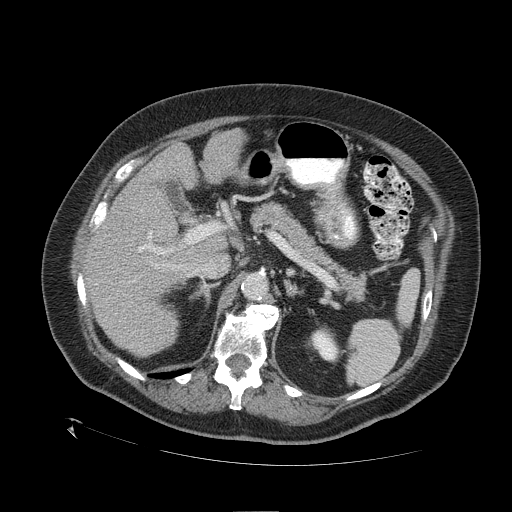
Contrast-enhanced abdominal CT (liver protocol), one axial slice; slice 66 of 109 in the series (ordered by position); reconstruction kernel STANDARD; one of 2 acquisitions stored at this slice position; soft-tissue window (W 400 / L 40 HU); 2.5 mm slice thickness; 512 × 512 image matrix. Case-level facts recorded for this patient, not image findings: diagnosis: hepatocellular carcinoma (patient treated with transarterial chemoembolisation; whether this scan precedes or follows treatment is not stated here); TNM stage (as recorded): Stage-I.
Annotated regions visible in this slice (semi-automatic segmentation, software-assisted and operator-edited):
- liver parenchyma outside the tumour (the mass and vessels are separate outlines, so this box may not span the whole liver): box from (x=84, y=128) to (x=245, y=356) px
- liver vessels: (x=96, y=217)–(x=195, y=267)